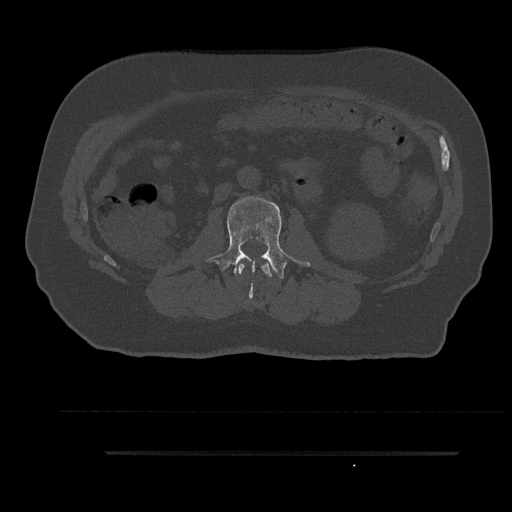
CT including the spine, one axial slice; reconstruction kernel Br40s/3; 120 kVp; bone window (W 1800 / L 400 HU); 512 × 512 image matrix, field of view 432 × 432 mm. Male patient, age 63 years. Case-level facts recorded for this patient, not image findings: primary cancer: renal.
Structures marked on this image (semi-automatic segmentation, software-assisted and operator-edited):
- L1 vertebra: box from (x=237, y=262) to (x=272, y=277) px
- L2 vertebra: (x=206, y=196)–(x=310, y=296)